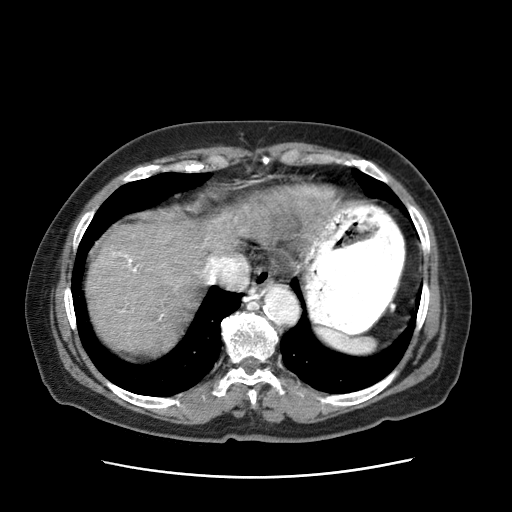
Contrast-enhanced abdominal CT (liver protocol), one axial slice; position 58 of 63 along the scan axis; reconstruction kernel STANDARD; 120 kVp; intravenous contrast given; soft-tissue window (W 400 / L 40 HU); 512 × 512 image matrix, field of view 360 × 360 mm. Female patient, age 79 years. Case-level facts recorded for this patient, not image findings: diagnosis: hepatocellular carcinoma (patient treated with transarterial chemoembolisation; whether this scan precedes or follows treatment is not stated here); TNM stage (as recorded): Stage-II.
Outlined on this slice (semi-automatic segmentation, software-assisted and operator-edited):
- abdominal aorta: bounding box [x1, y1, x2, y2] px = [262, 287, 298, 325]
- liver parenchyma outside the tumour (the mass and vessels are separate outlines, so this box may not span the whole liver): [90, 208, 238, 359]
- mass: [229, 183, 335, 243]
- liver vessels: [124, 253, 250, 320]